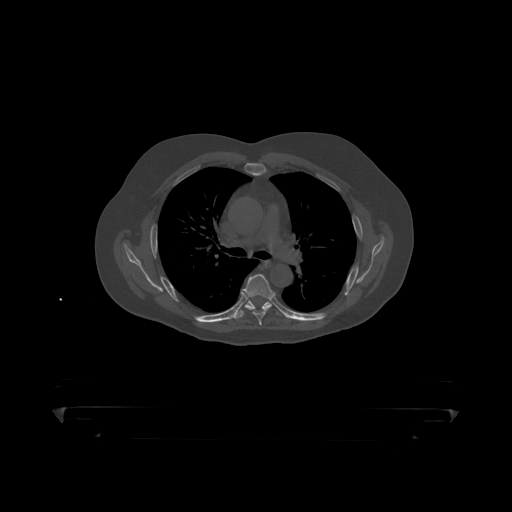
CT including the spine, one axial slice; position 312 of 390 along the scan axis; bone window (W 1800 / L 400 HU); 1.25 mm slice thickness; 512 × 512 image matrix, field of view 650 × 650 mm. Male patient, age 60 years. Case-level facts recorded for this patient, not image findings: primary cancer: prostate.
Outlined on this slice (semi-automatically segmented with operator editing):
- T5 vertebra: bounding box (x1, y1, x2, y2) in pixels: (242, 275, 274, 319)
- T6 vertebra: (235, 300, 280, 317)